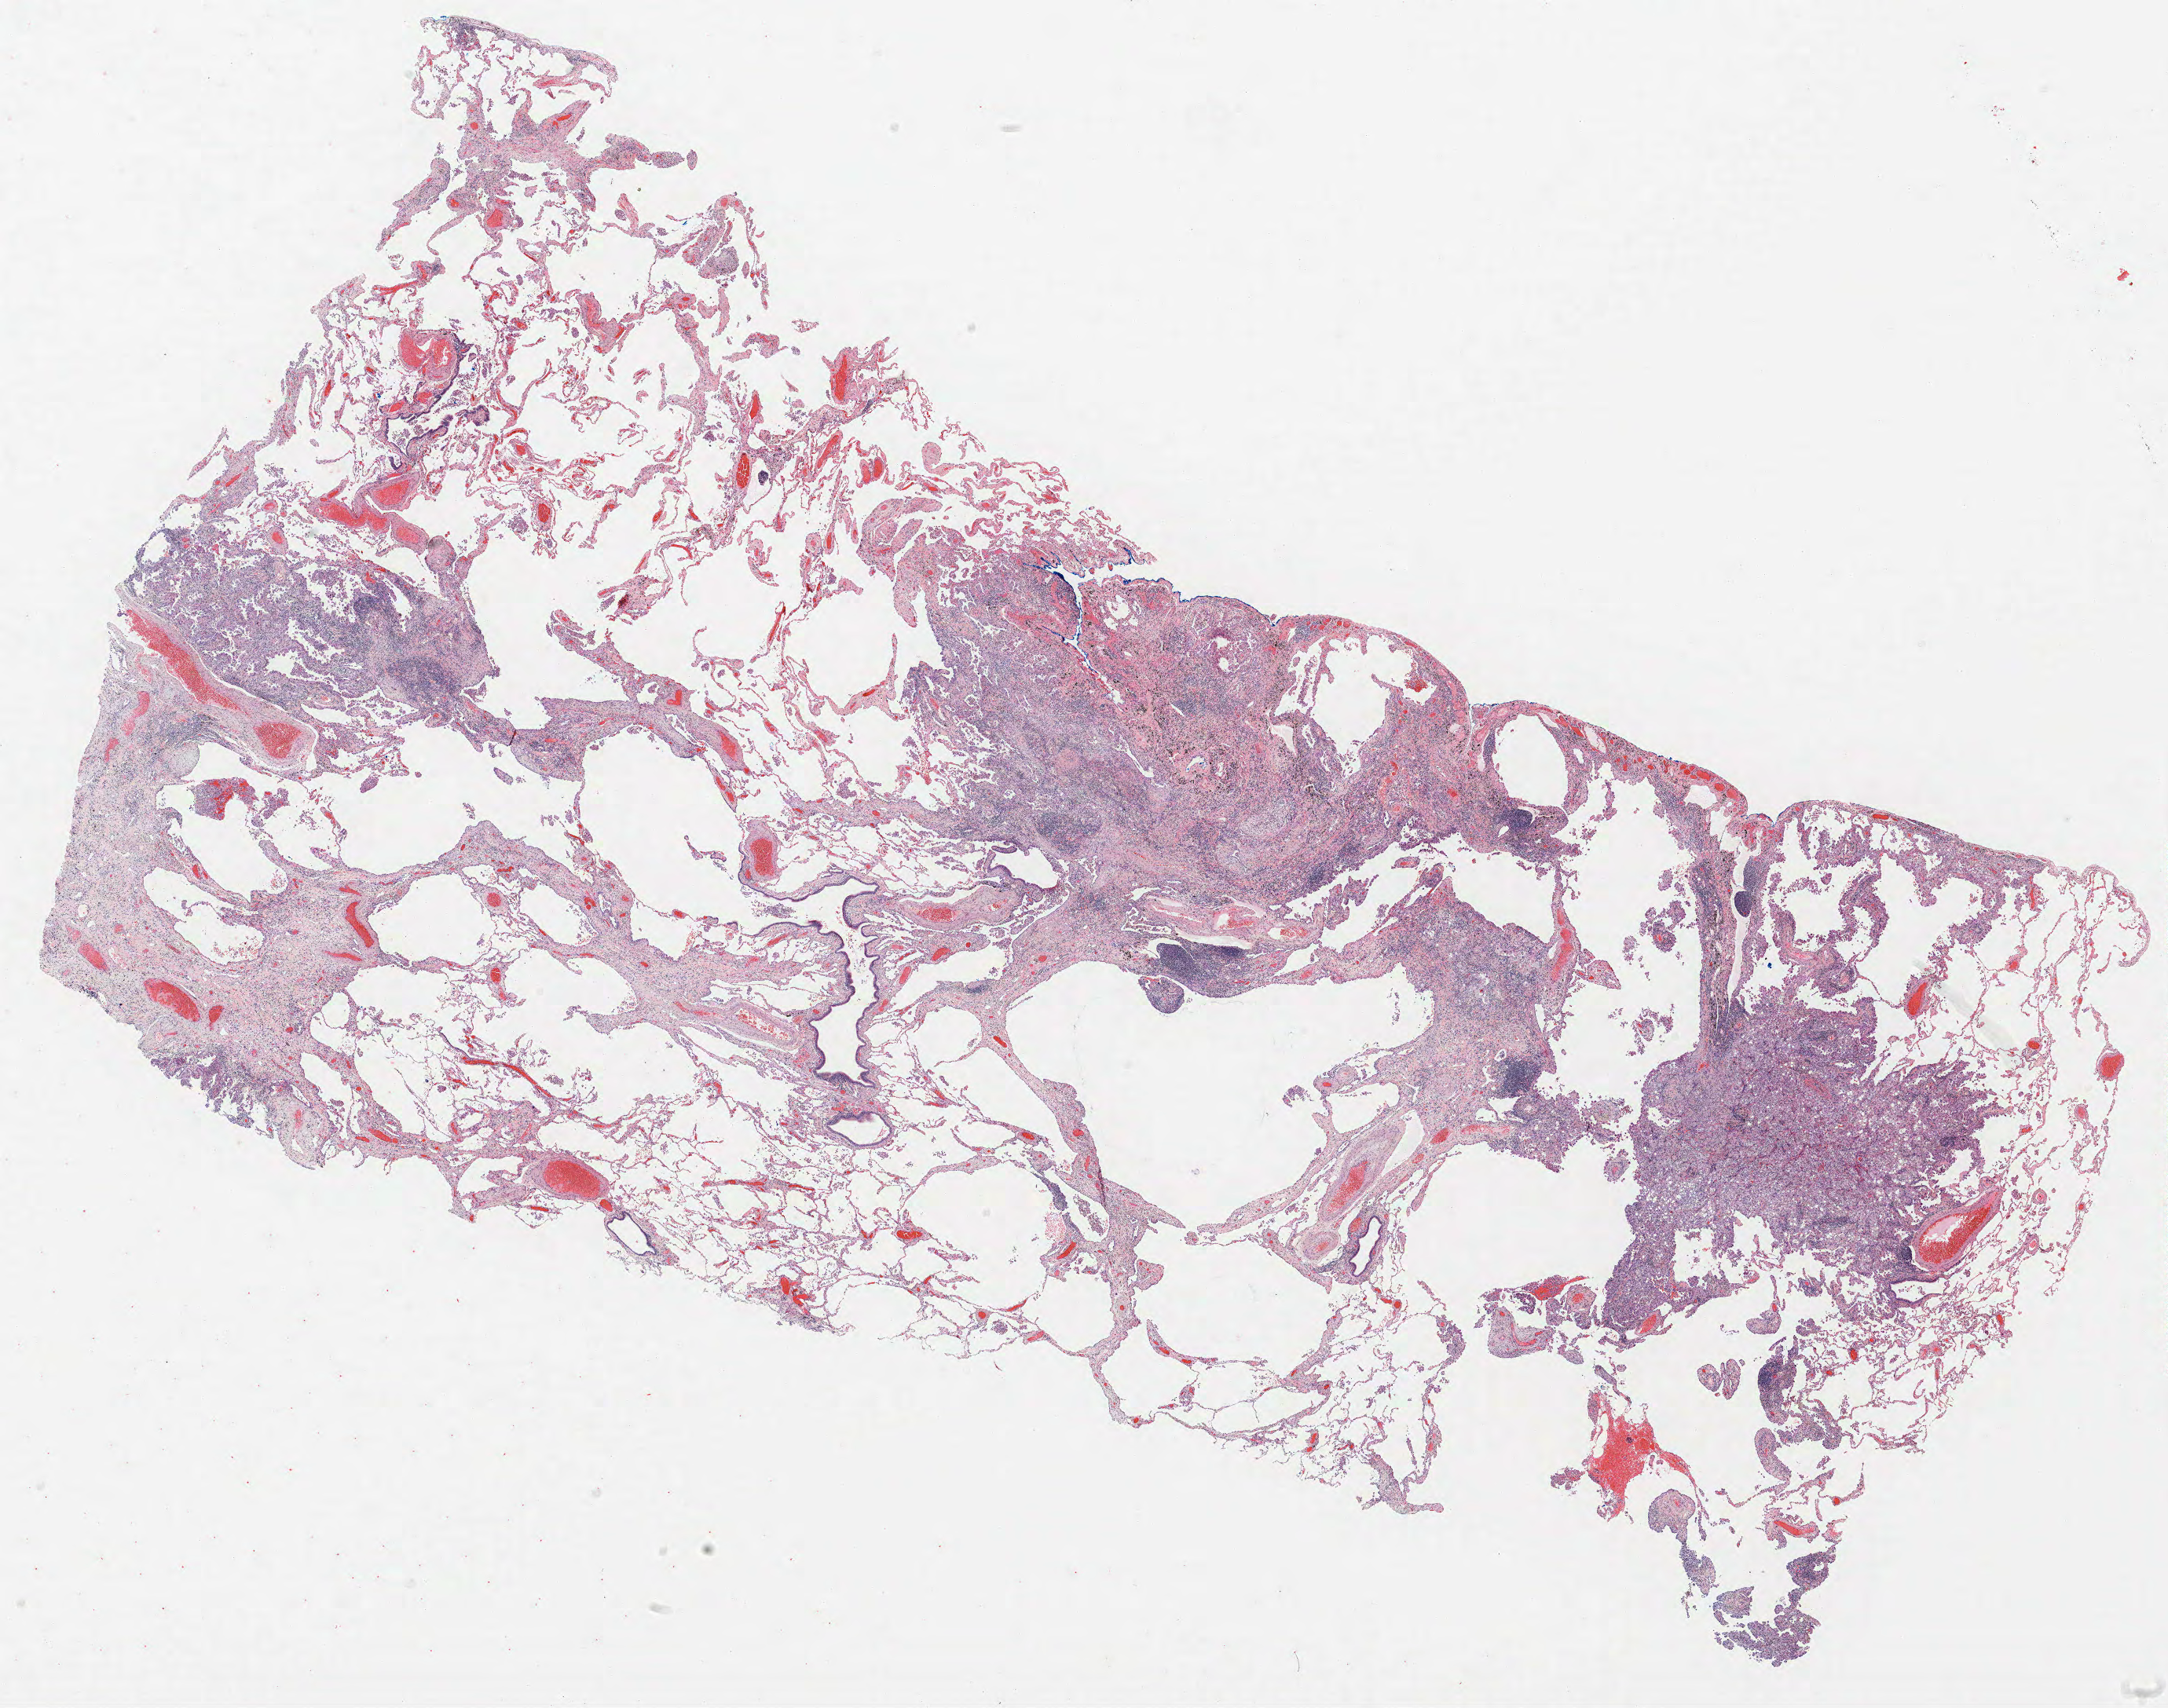
Hematoxylin and eosin (H&E) stained whole-slide image — shown as a low-resolution overview of the whole scanned area (about 22.1 x 17.4 mm). Formalin-fixed paraffin-embedded (FFPE) section. Lung. Female, age 61 at enrolment. Current smoker at enrolment. Grade: poorly differentiated (G3).
• stage (AJCC 6th edition): IB
• primary tumour location (clinical record): left lower lobe
• tumour size (pathology): 100 mm
• participant's lung-cancer diagnosis: Non-small cell carcinoma